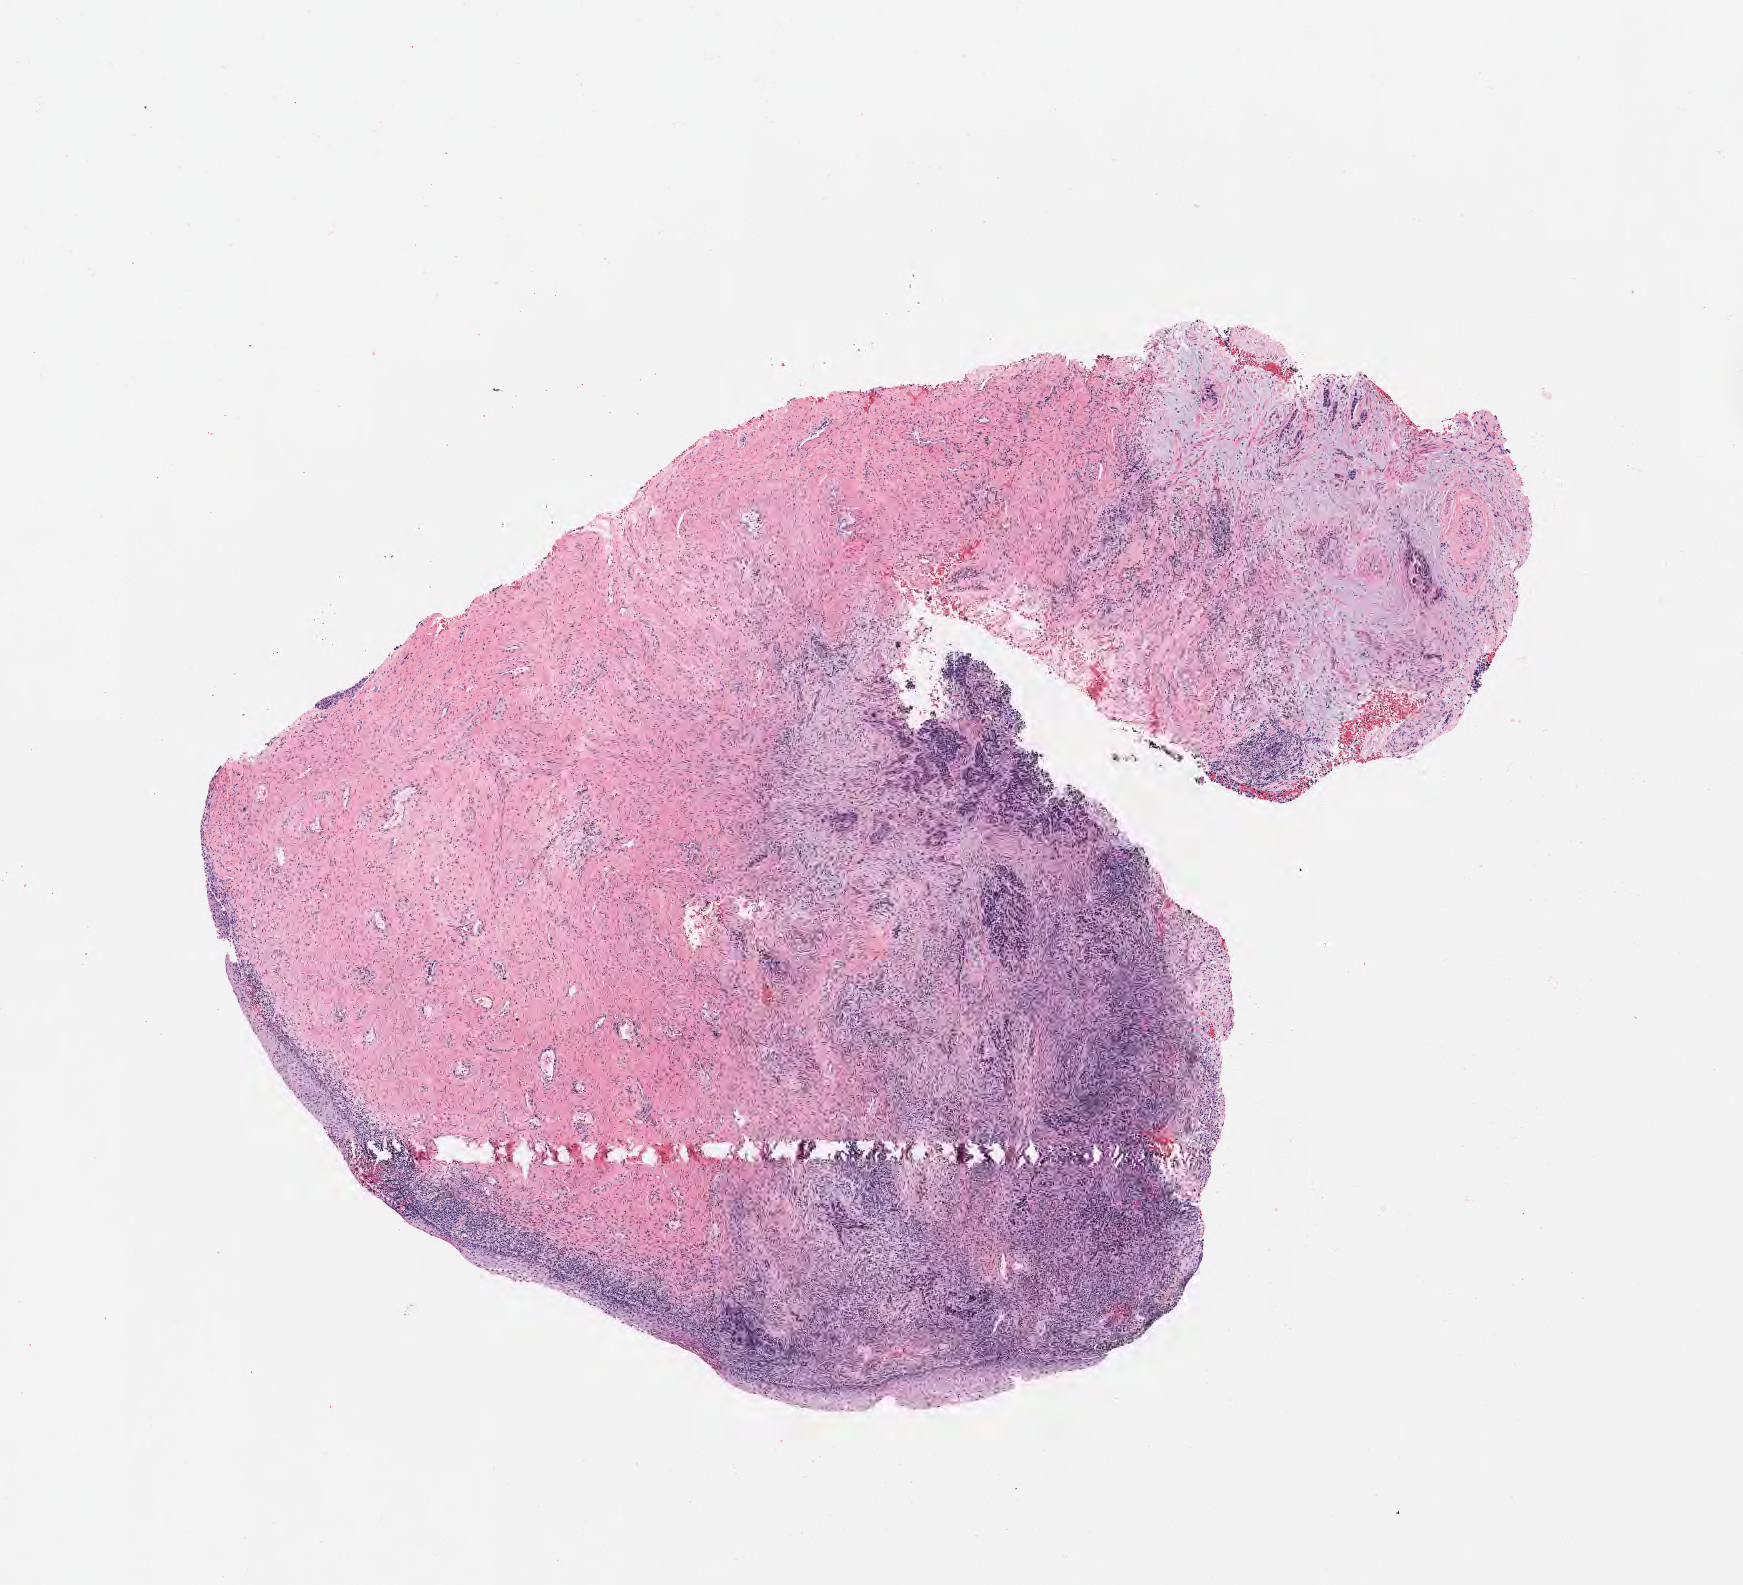
Digitized hematoxylin and eosin (H&E)-stained section, shown as a low-resolution overview of the whole scanned area (about 7.0 x 6.4 mm); specimen: tumor tissue; site: cervix. Female patient, 68 years old.
• diagnosis: Squamous cell carcinoma, large cell, nonkeratinizing, NOS